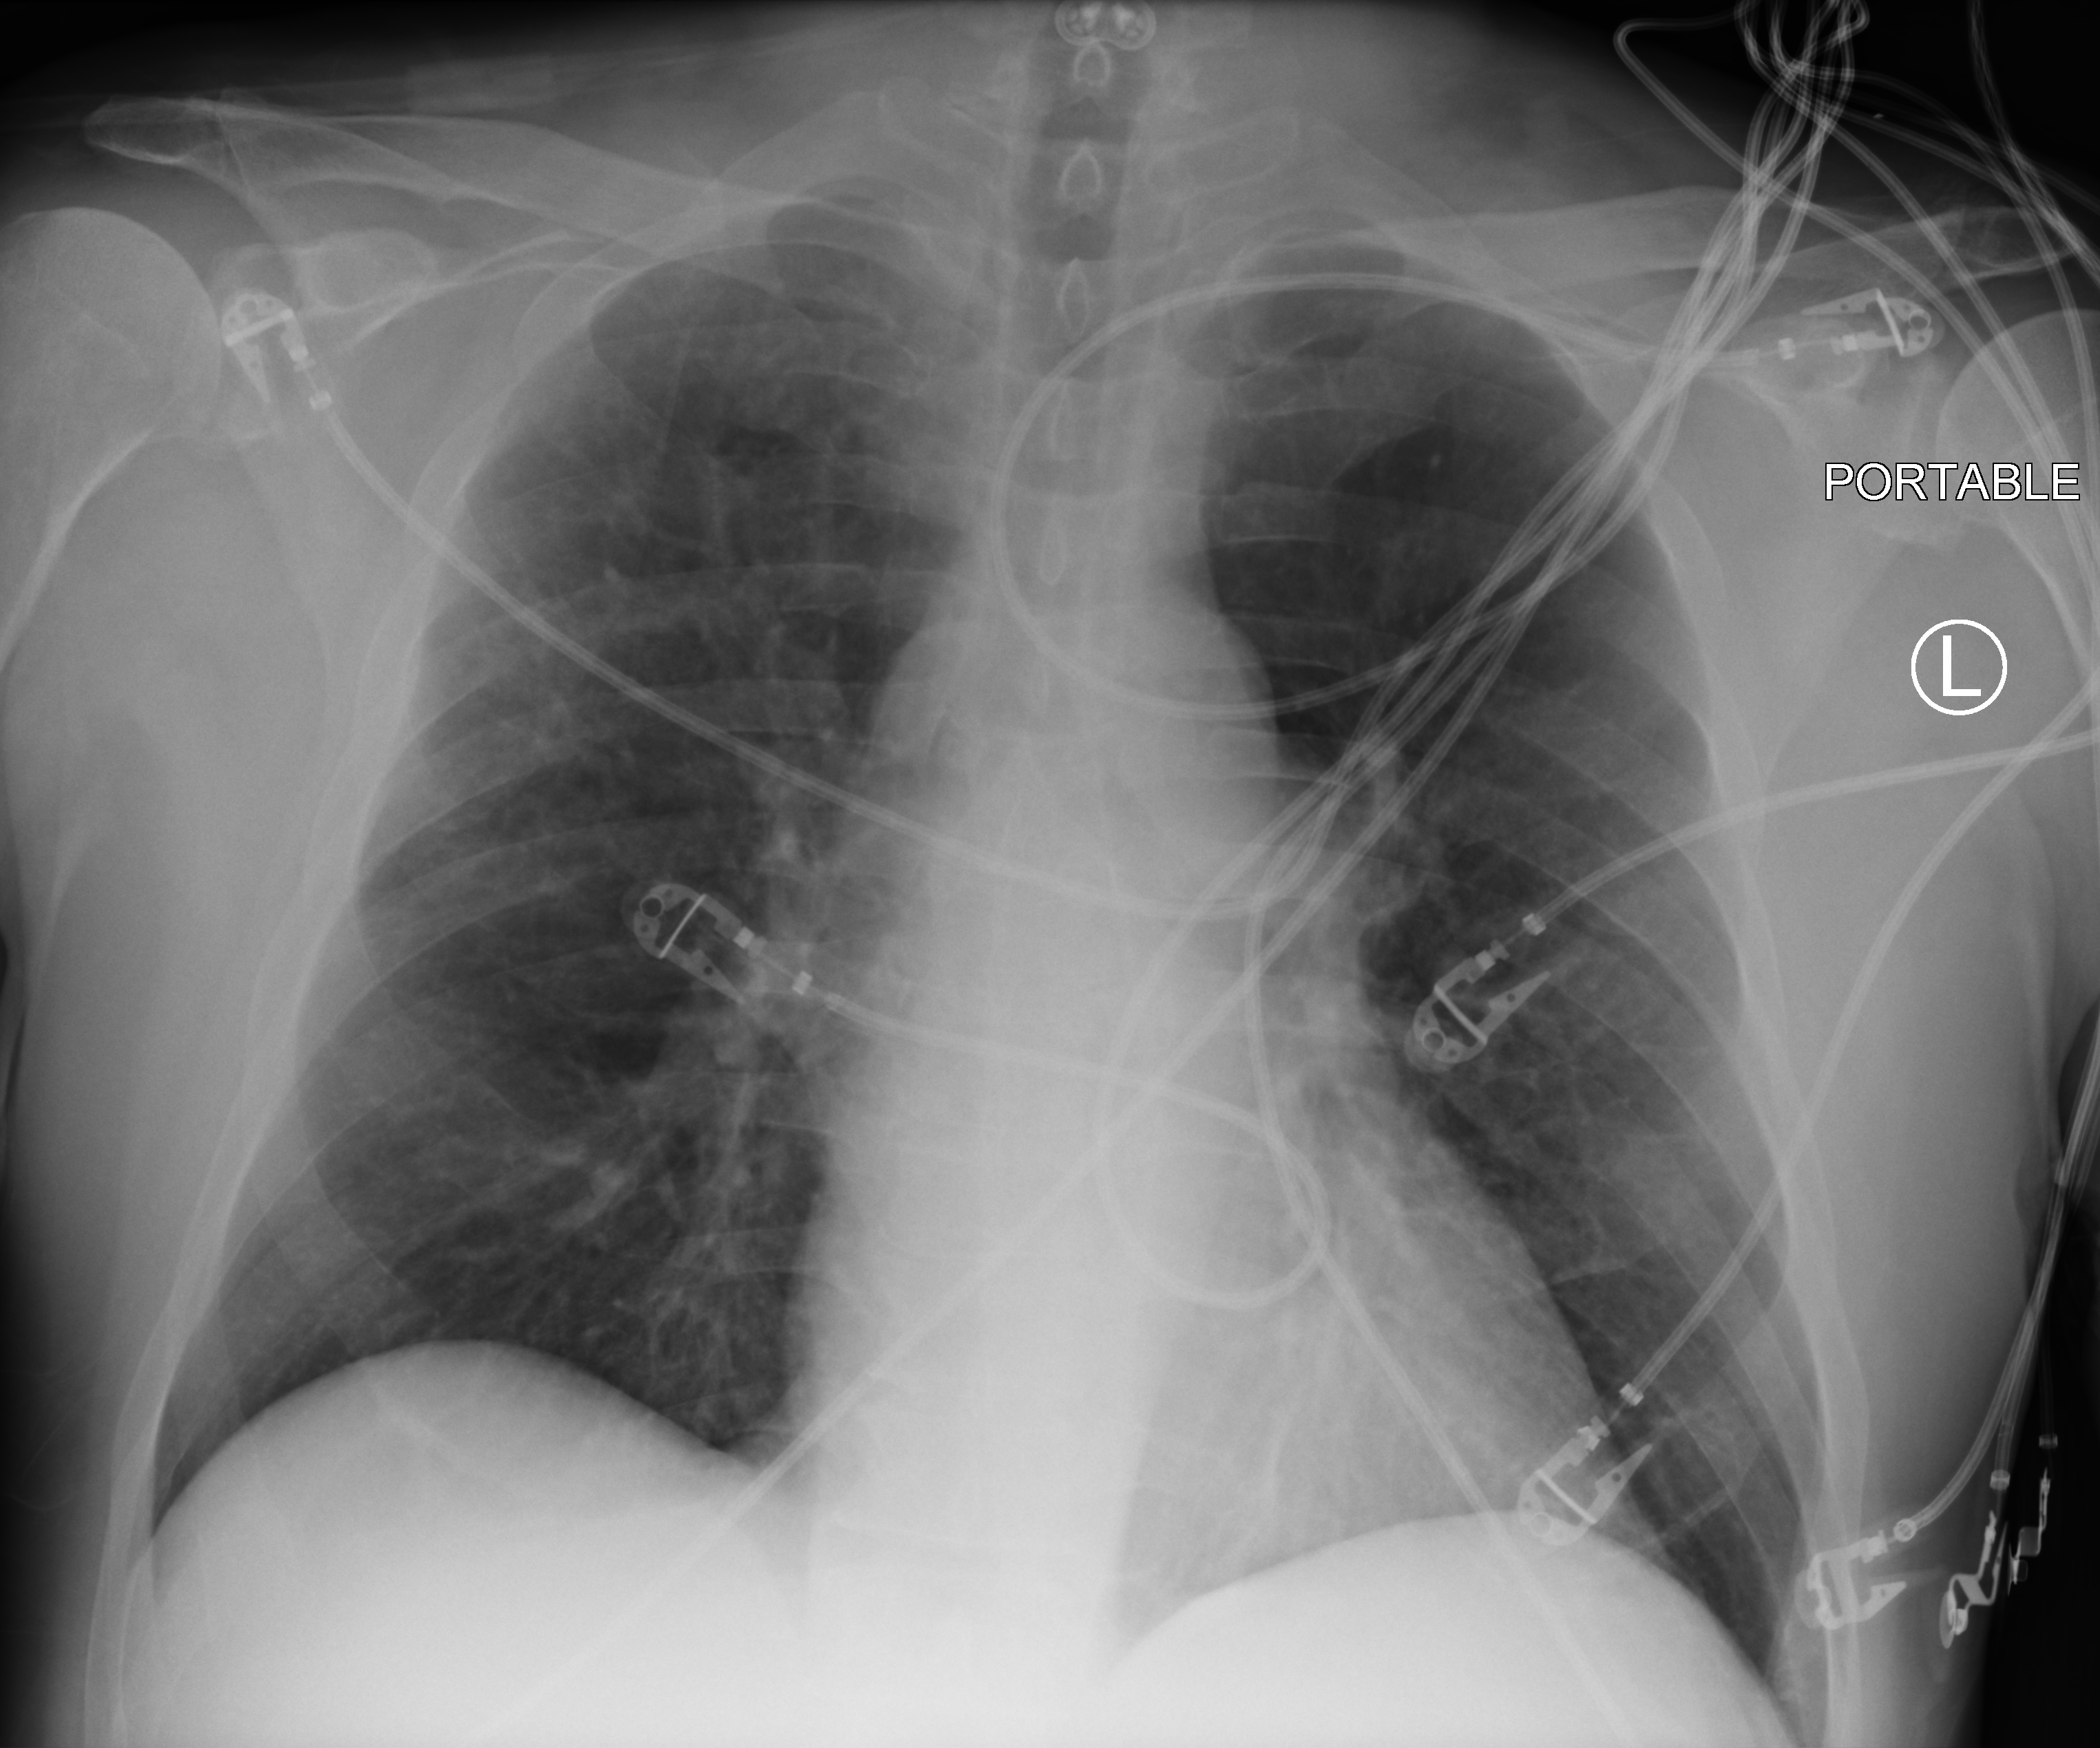
Portable chest radiograph. Patient hospitalised with COVID-19; male, aged 60–74 years.
From the hospital-stay record, not from the radiograph (when in the stay this image was taken is not recorded): chronic kidney disease (admission record): no; smoking status (admission record): former; admitted to intensive care during this hospital stay: no.